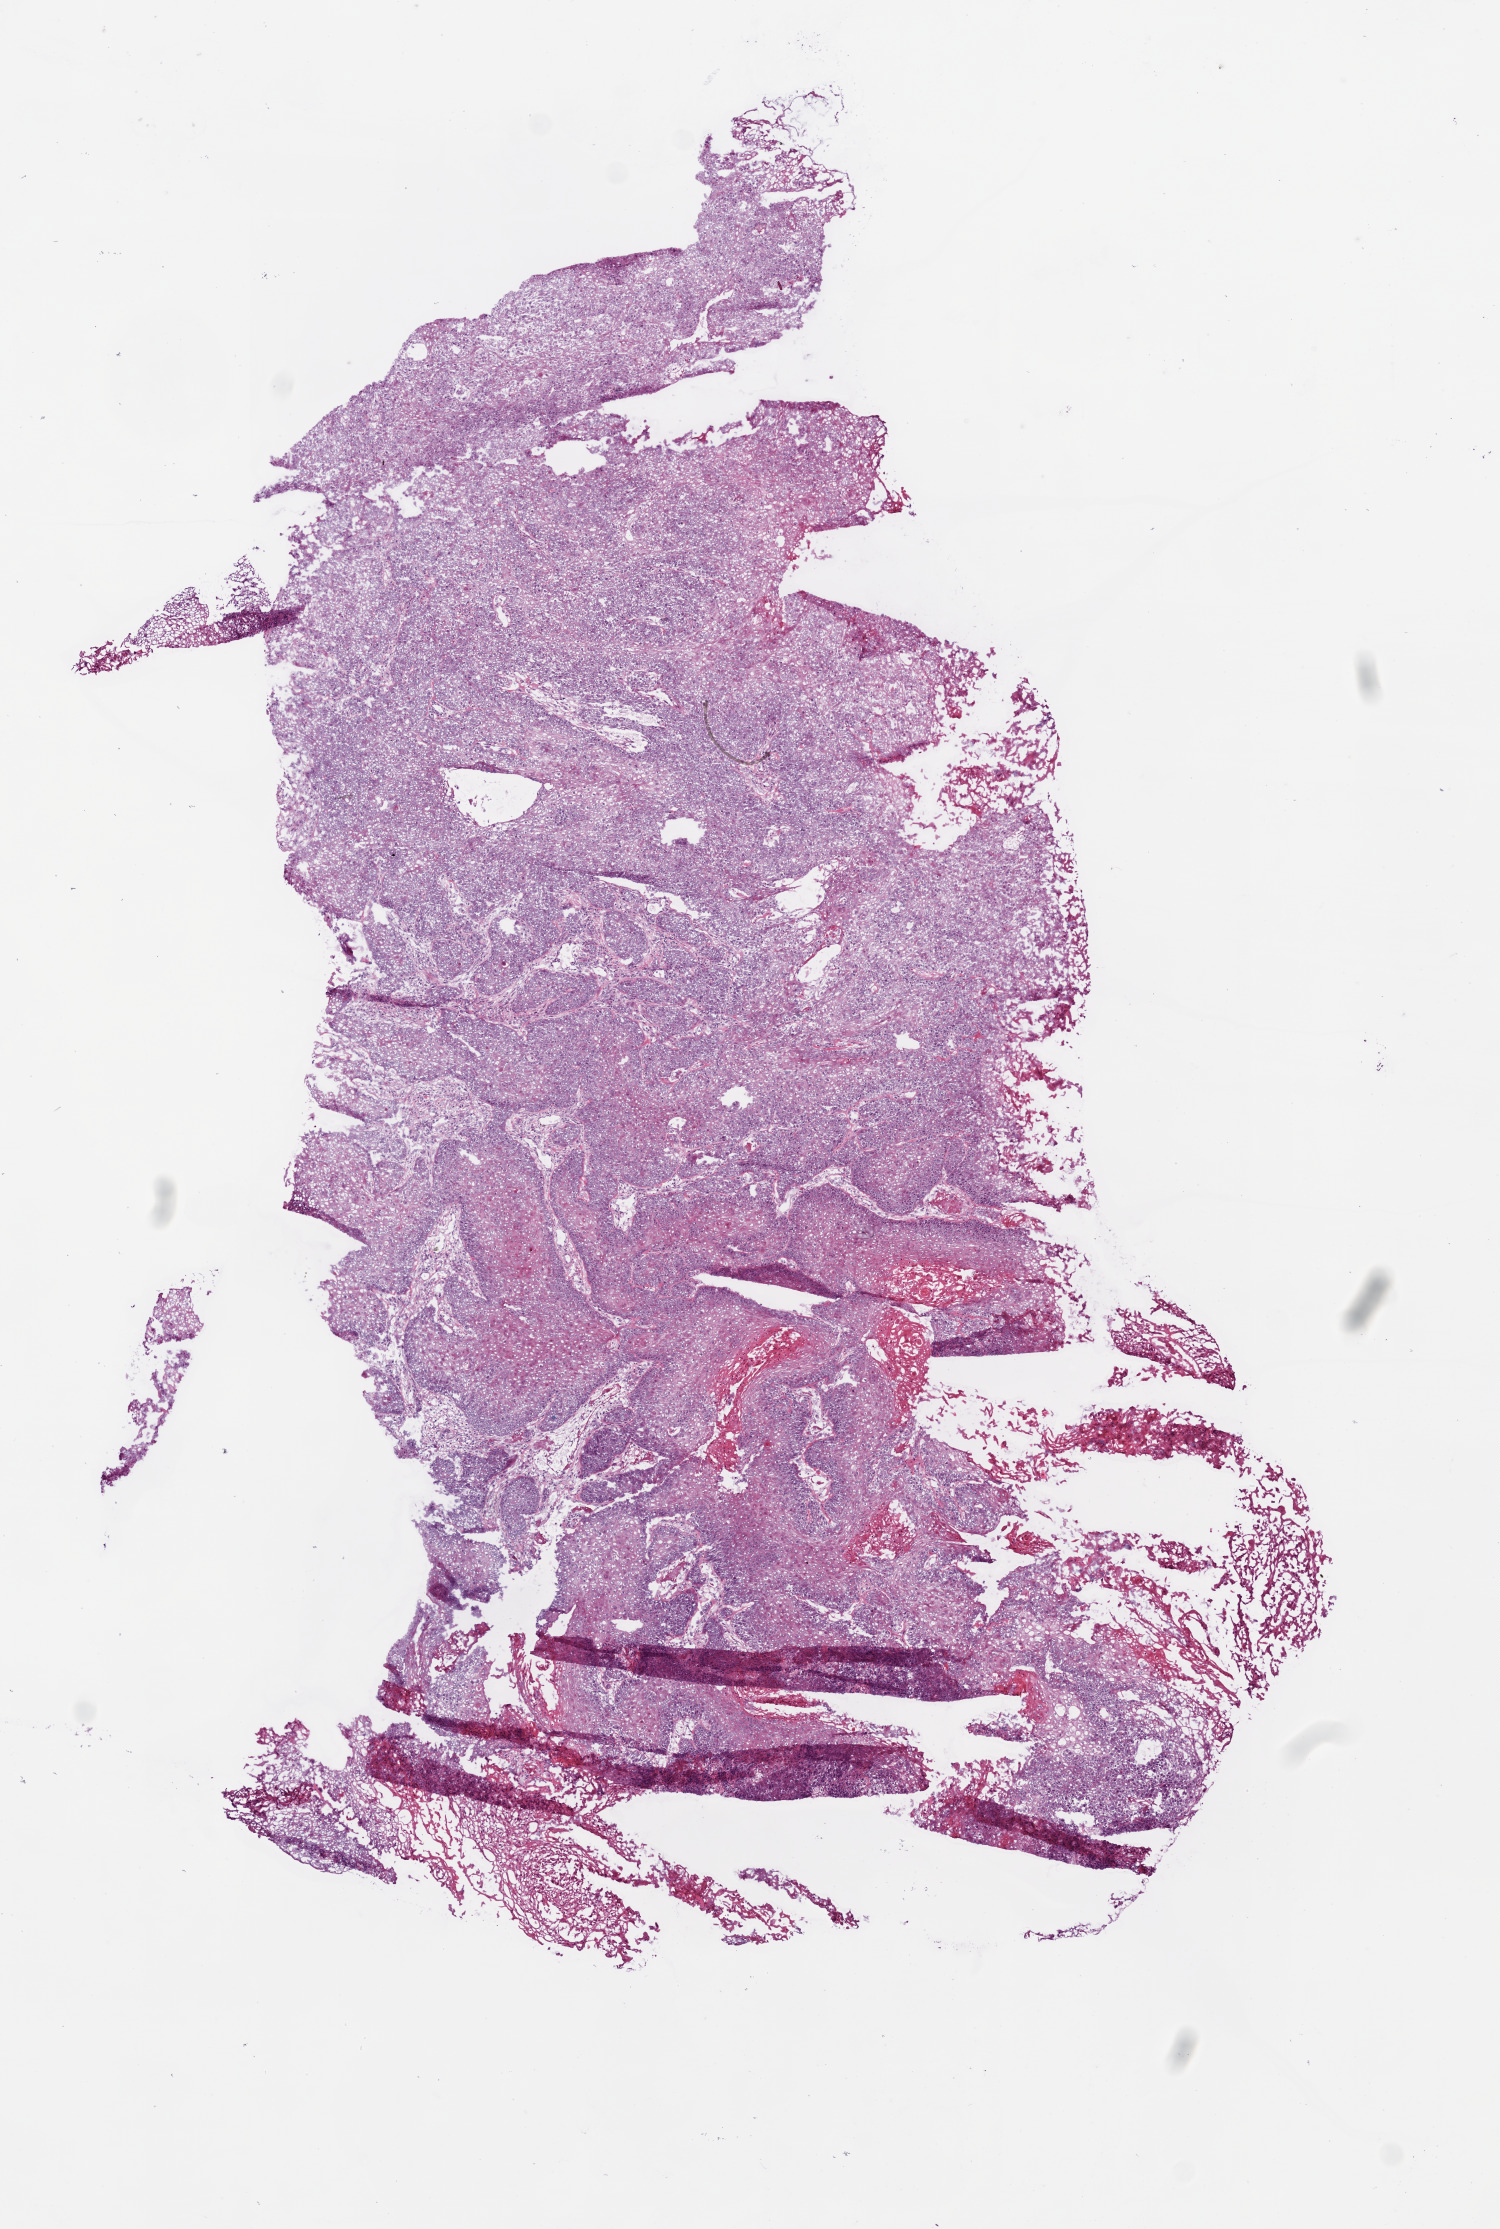
Whole-slide histology image, H&E-stained, low-resolution overview of the scanned area, about 6.0 x 8.9 mm, frozen section, sample: primary tumour, head and neck. Male, age 39 years at initial diagnosis. Histologic grade: G2 (moderately differentiated). Composition of this section per pathologist review: tumour cells 95%, tumour nuclei 90%, normal cells 0%, stromal cells 3%, necrosis 2%.
- diagnosis: Squamous cell carcinoma, NOS